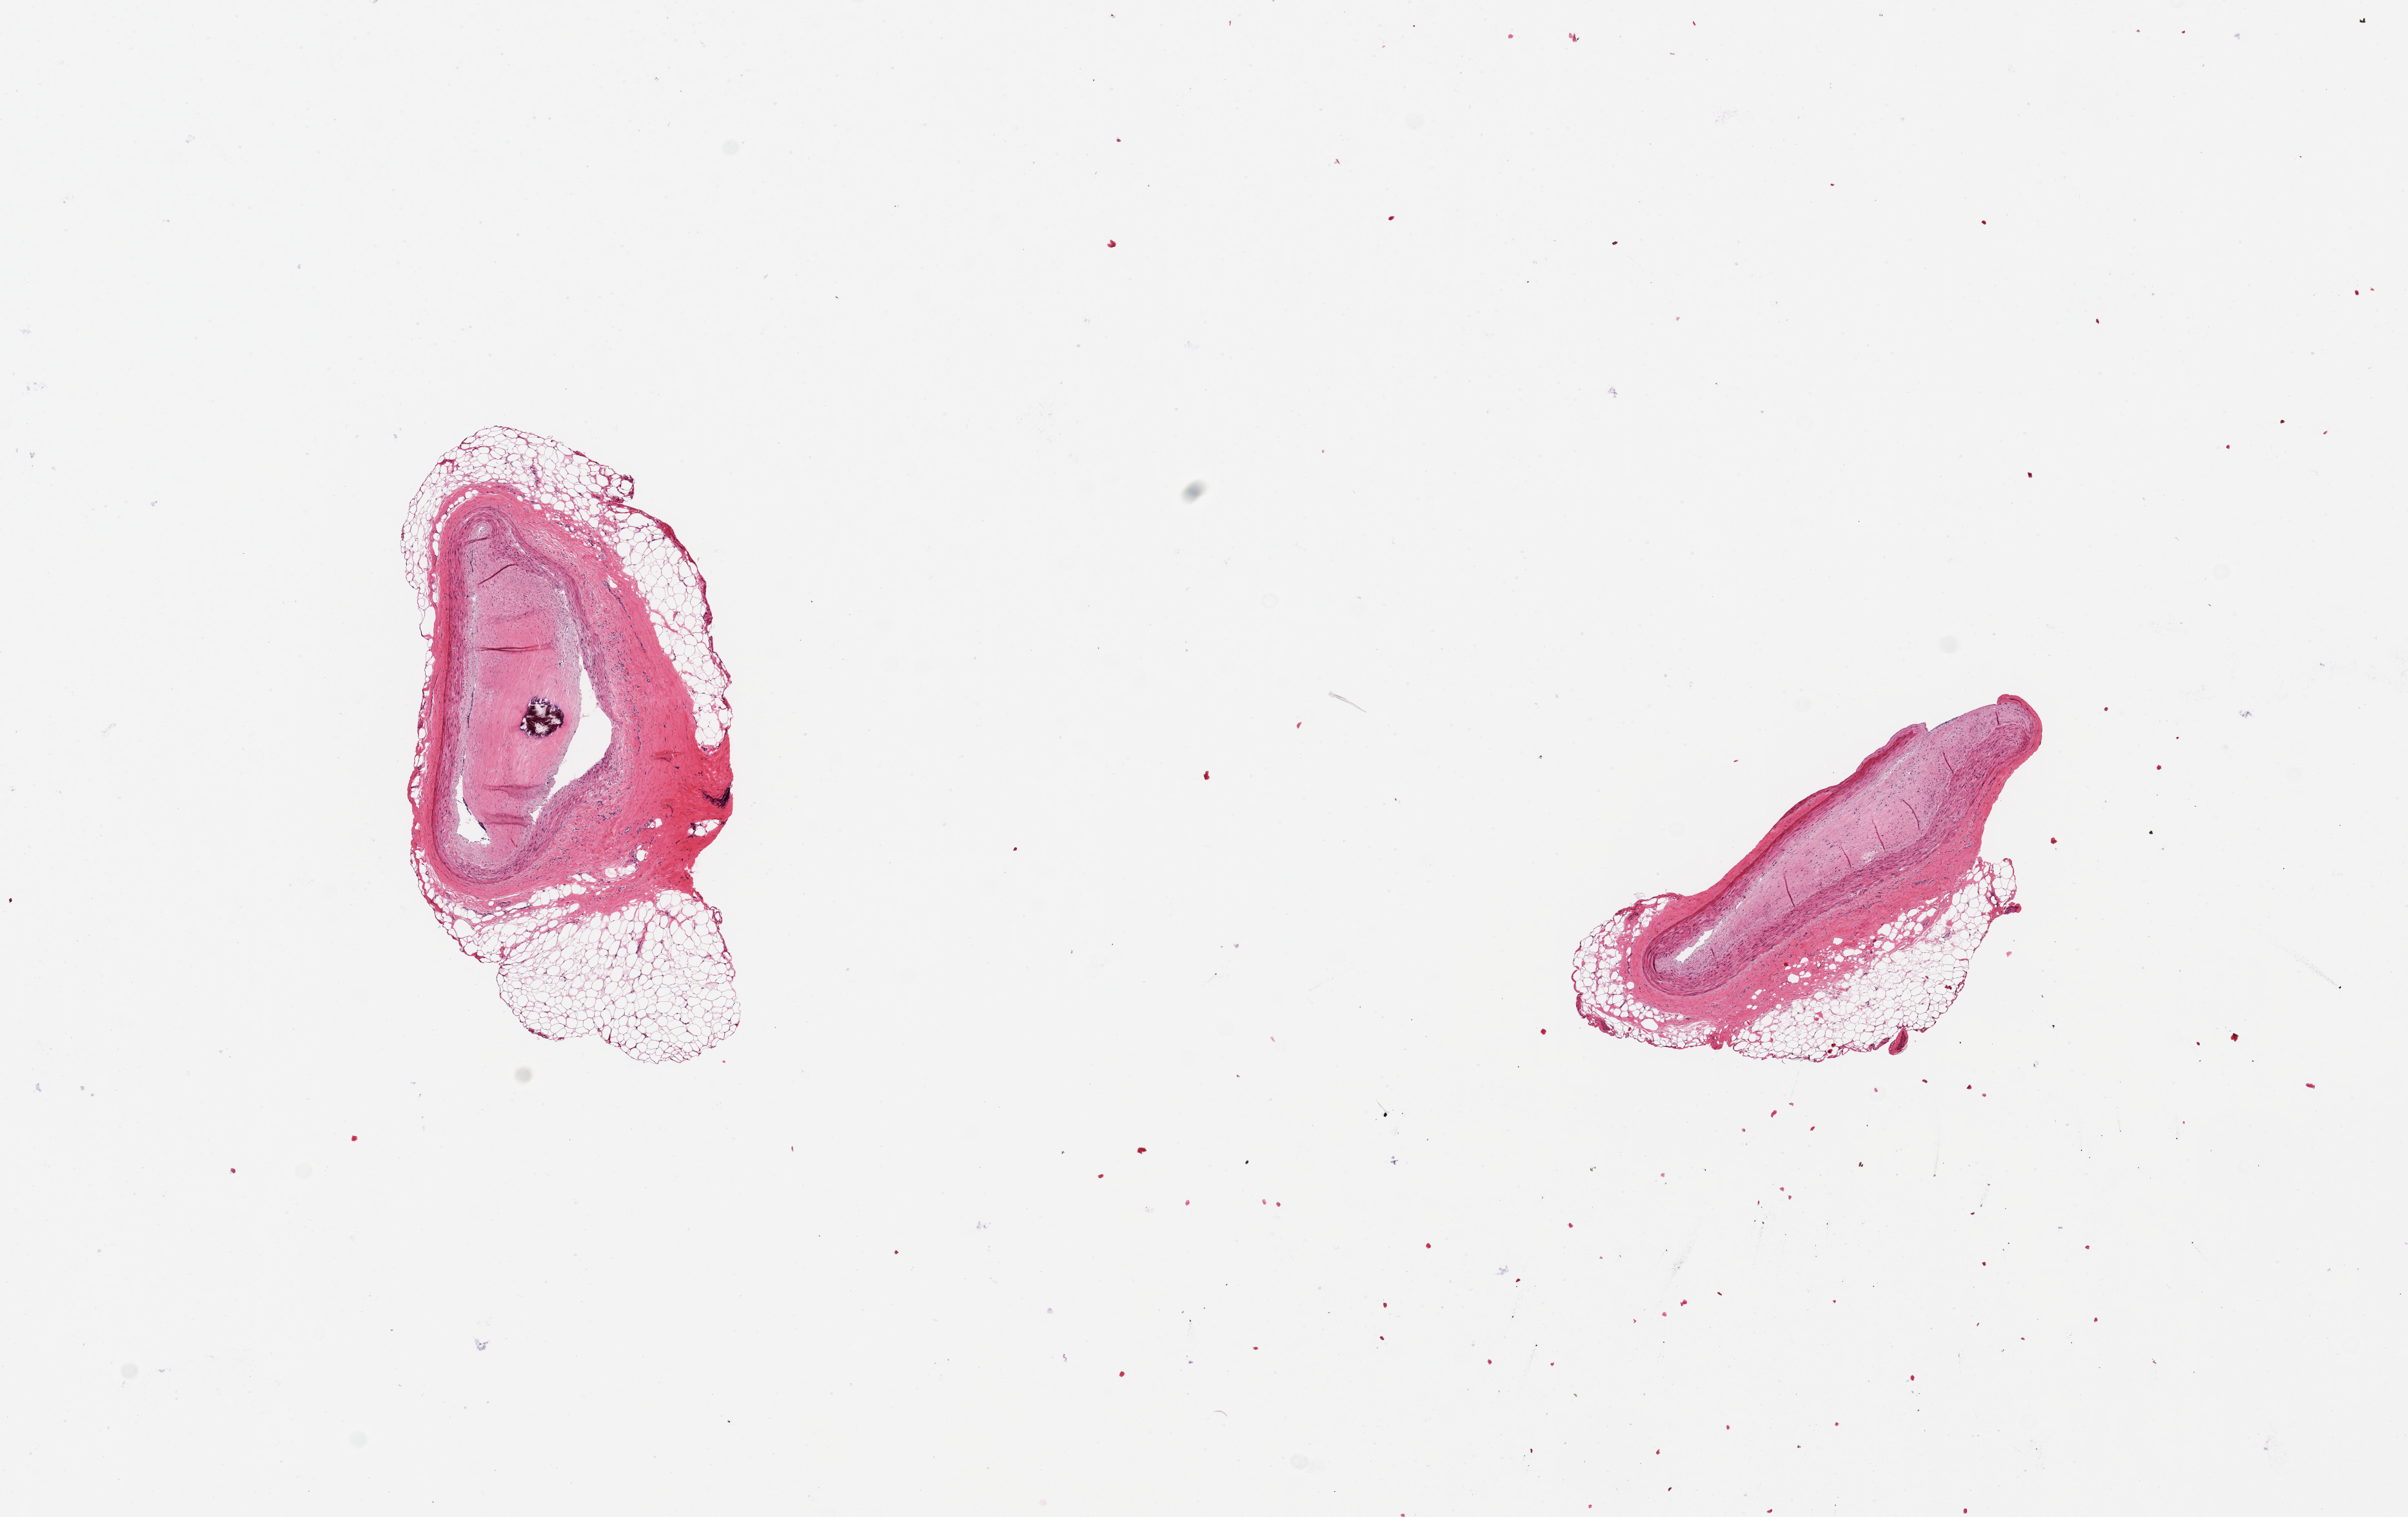
Whole-slide image, haematoxylin and eosin stain, brightfield, whole scanned area (about 14.8 x 9.3 mm, acquisition: 20x scan) shown as a low-resolution overview. PAXgene-fixed paraffin-embedded (PFPE) section. Section of coronary artery (target tissue). Donor tissue sample. Donor sex: male.
Review note (as recorded): 2 pieces, 4x2 & 3x2mm; Occlusive fibrocalcific plaque. 40% extraneous adipose.